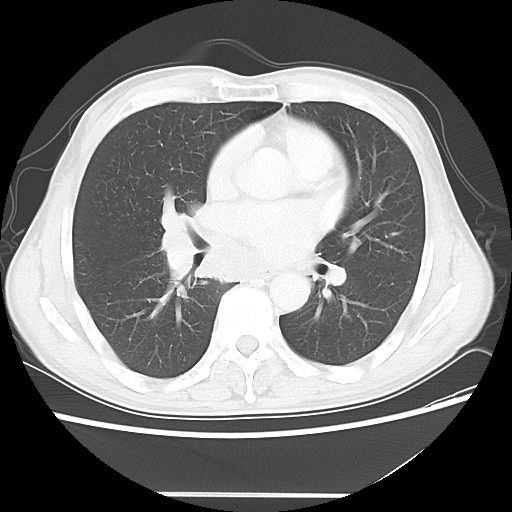
Chest CT, one axial slice; position 27 of 56 along the scan axis; 120 kVp; lung window (W 1500 / L -600 HU); 512 × 512 image matrix, field of view 344 × 344 mm. Patient: male, 65 years. Case-level facts recorded for this patient, not image findings: clinical TNM (as recorded): T1c N3 M0.
Annotated regions visible in this slice (rectangle marked by the reading radiologist):
- lung tumour (recorded histology: small cell carcinoma): bounding box <153,194,201,294> (left, top, right, bottom; pixels)